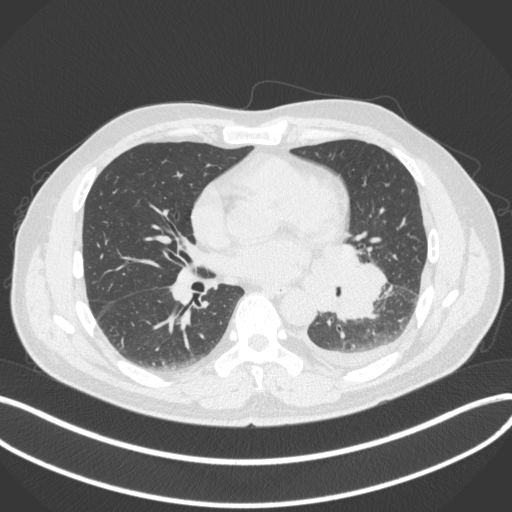
Chest CT, one axial slice; position 172 of 350 along the scan axis; reconstruction kernel B31f; 120 kVp; lung window (W 1500 / L -600 HU); 1 mm slice thickness; 512 × 512 image matrix, field of view 400 × 400 mm. Male patient, age 58 years. Case-level facts recorded for this patient, not image findings: clinical TNM (as recorded): T3 N1 M1b; histopathological grade: G3.
Structures marked on this image (bounding box drawn by a radiologist):
- lung tumour (recorded histology: small cell carcinoma): box from (x=315, y=243) to (x=388, y=323) px